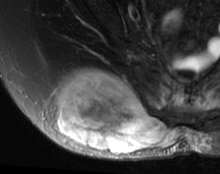
MRI of an extremity soft-tissue mass, one axial slice; position 32 of 63 along the scan axis; T2-weighted fat-saturated; MR volume resampled by the dataset authors to the PET/CT grid (not the native acquisition matrix); 3.27 mm slice thickness; 220 × 174 image matrix, field of view 215 × 170 mm. Female patient. Case-level facts recorded for this patient, not image findings: histological type: spindle cell suggestive of myxofibrosarcoma; grade: intermediate; site of the primary tumour: right buttock.
Structures marked on this image (expert contour drawn on MRI and transferred to this co-registered scan by the dataset authors):
- gross tumour volume (mass): bounding box [x1, y1, x2, y2] px = [56, 70, 181, 156]